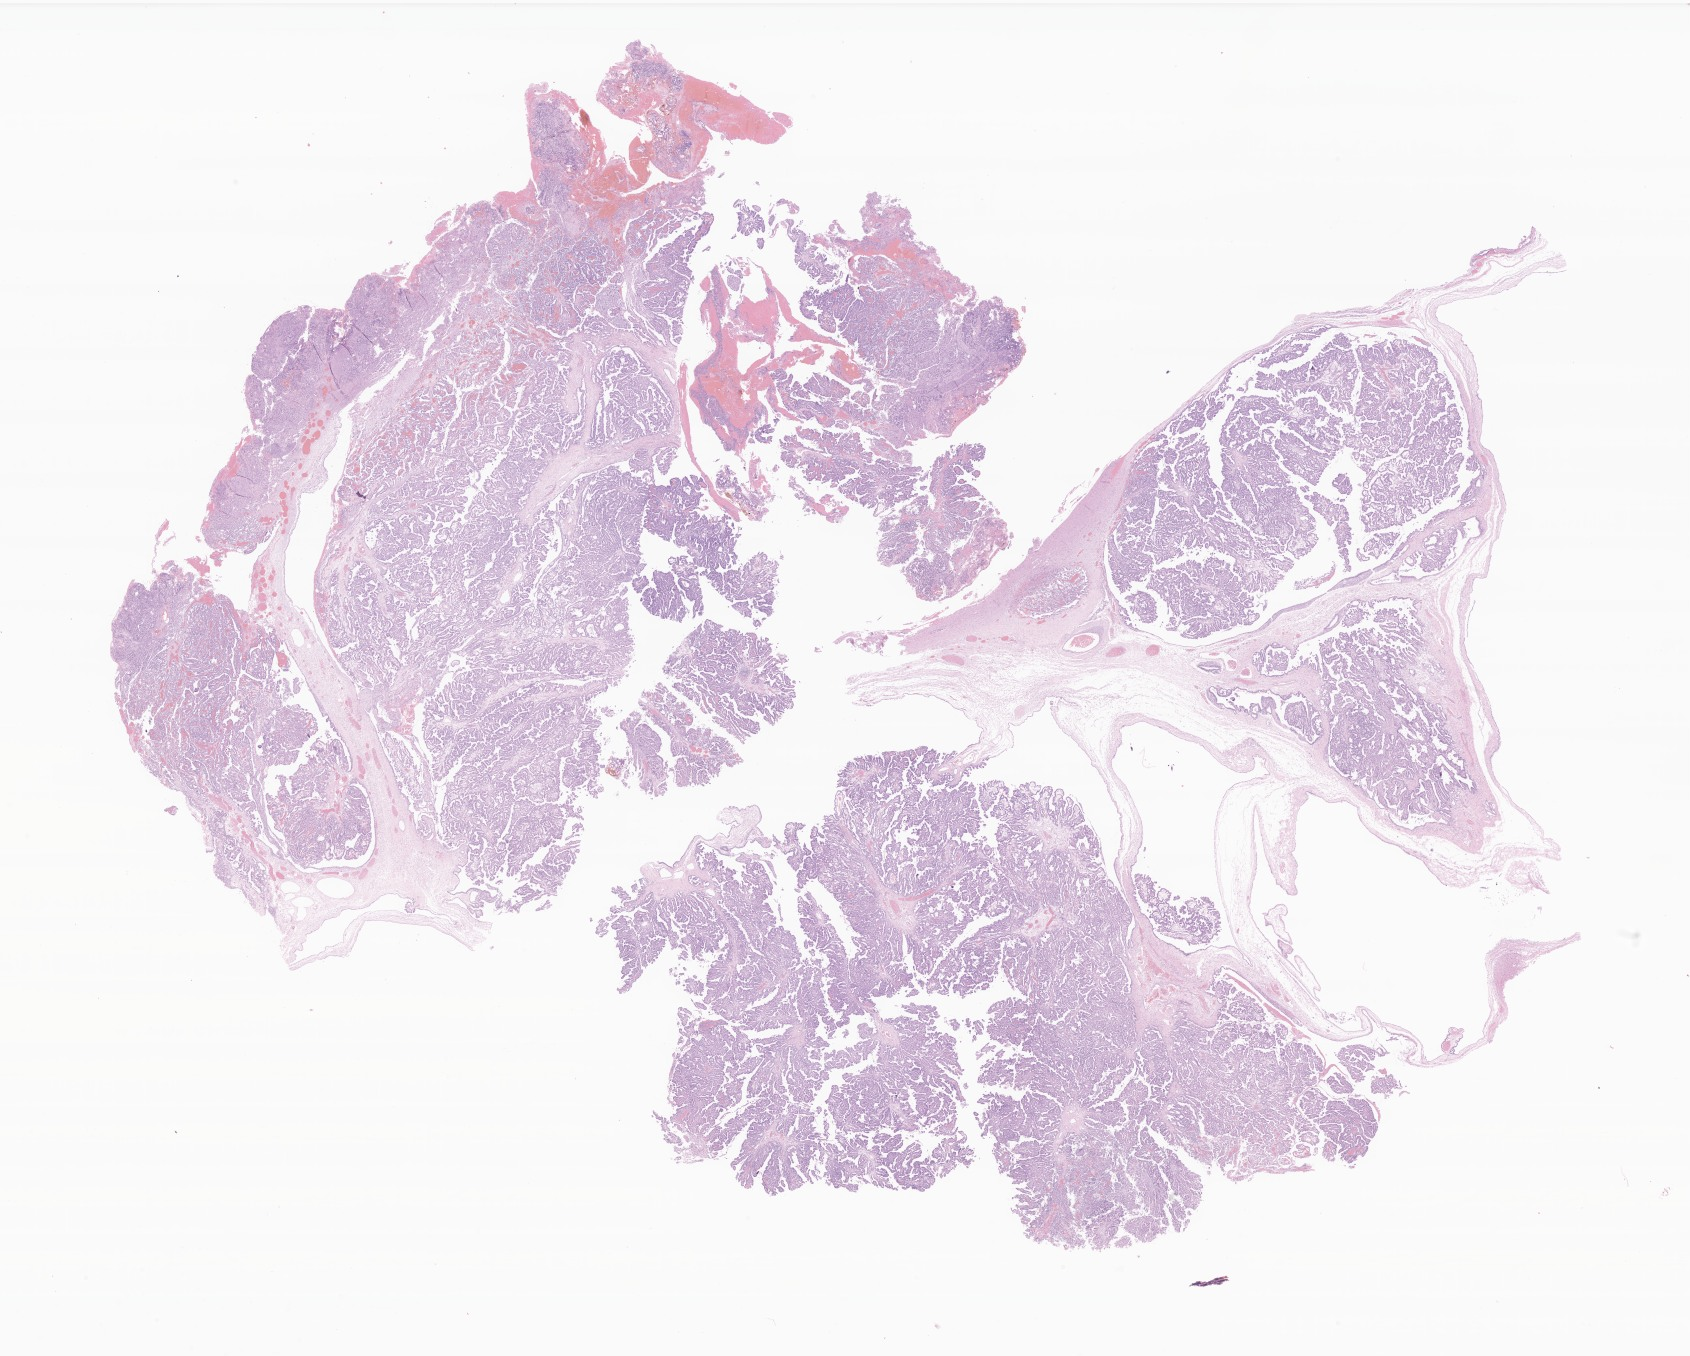
Whole-slide image, haematoxylin and eosin stain of tumor tissue from the brain — shown as a low-resolution overview of the whole scanned area (about 28.5 x 22.9 mm). FFPE section. Patient female; age 228 days.
Diagnosis (ICD-O-3 morphology term): Atypical choroid plexus papilloma.